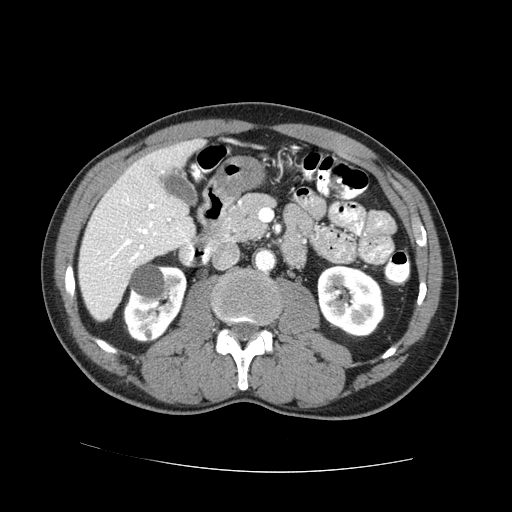
Contrast-enhanced abdominal CT (liver protocol), one axial slice; slice 25 of 73 in the series (ordered by position); reconstruction kernel STANDARD; 100 kVp; one of 2 acquisitions stored at this slice position; soft-tissue window (W 400 / L 40 HU); 512 × 512 image matrix, field of view 380 × 380 mm. From the clinical record (not read from this slice): diagnosis: hepatocellular carcinoma (patient treated with transarterial chemoembolisation; whether this scan precedes or follows treatment is not stated here); TNM stage (as recorded): Stage-IVA; Child-Pugh class: A; tumour differentiation: no biopsy; tumour nodularity: uninodular.
Annotated regions visible in this slice (semi-automatic segmentation, software-assisted and operator-edited):
- liver parenchyma outside the tumour (the mass and vessels are separate outlines, so this box may not span the whole liver): box from (x=78, y=138) to (x=204, y=320) px
- liver vessels: (x=98, y=199)–(x=187, y=265)